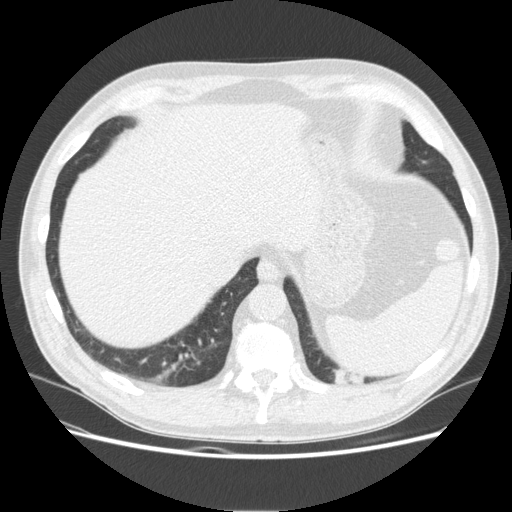
Low-dose screening chest CT, one axial slice. Position 41 of 165 along the scan axis. Reconstruction kernel STANDARD. 120 kVp. Lung window (W 1500 / L -600 HU). 2.5 mm slice thickness. 512 × 512 image matrix.
Structures marked on this image (outlined manually by an expert reader):
- lesion 1 (tumor, upper lobe of left lung): bounding box <333,370,365,384> (left, top, right, bottom; pixels)